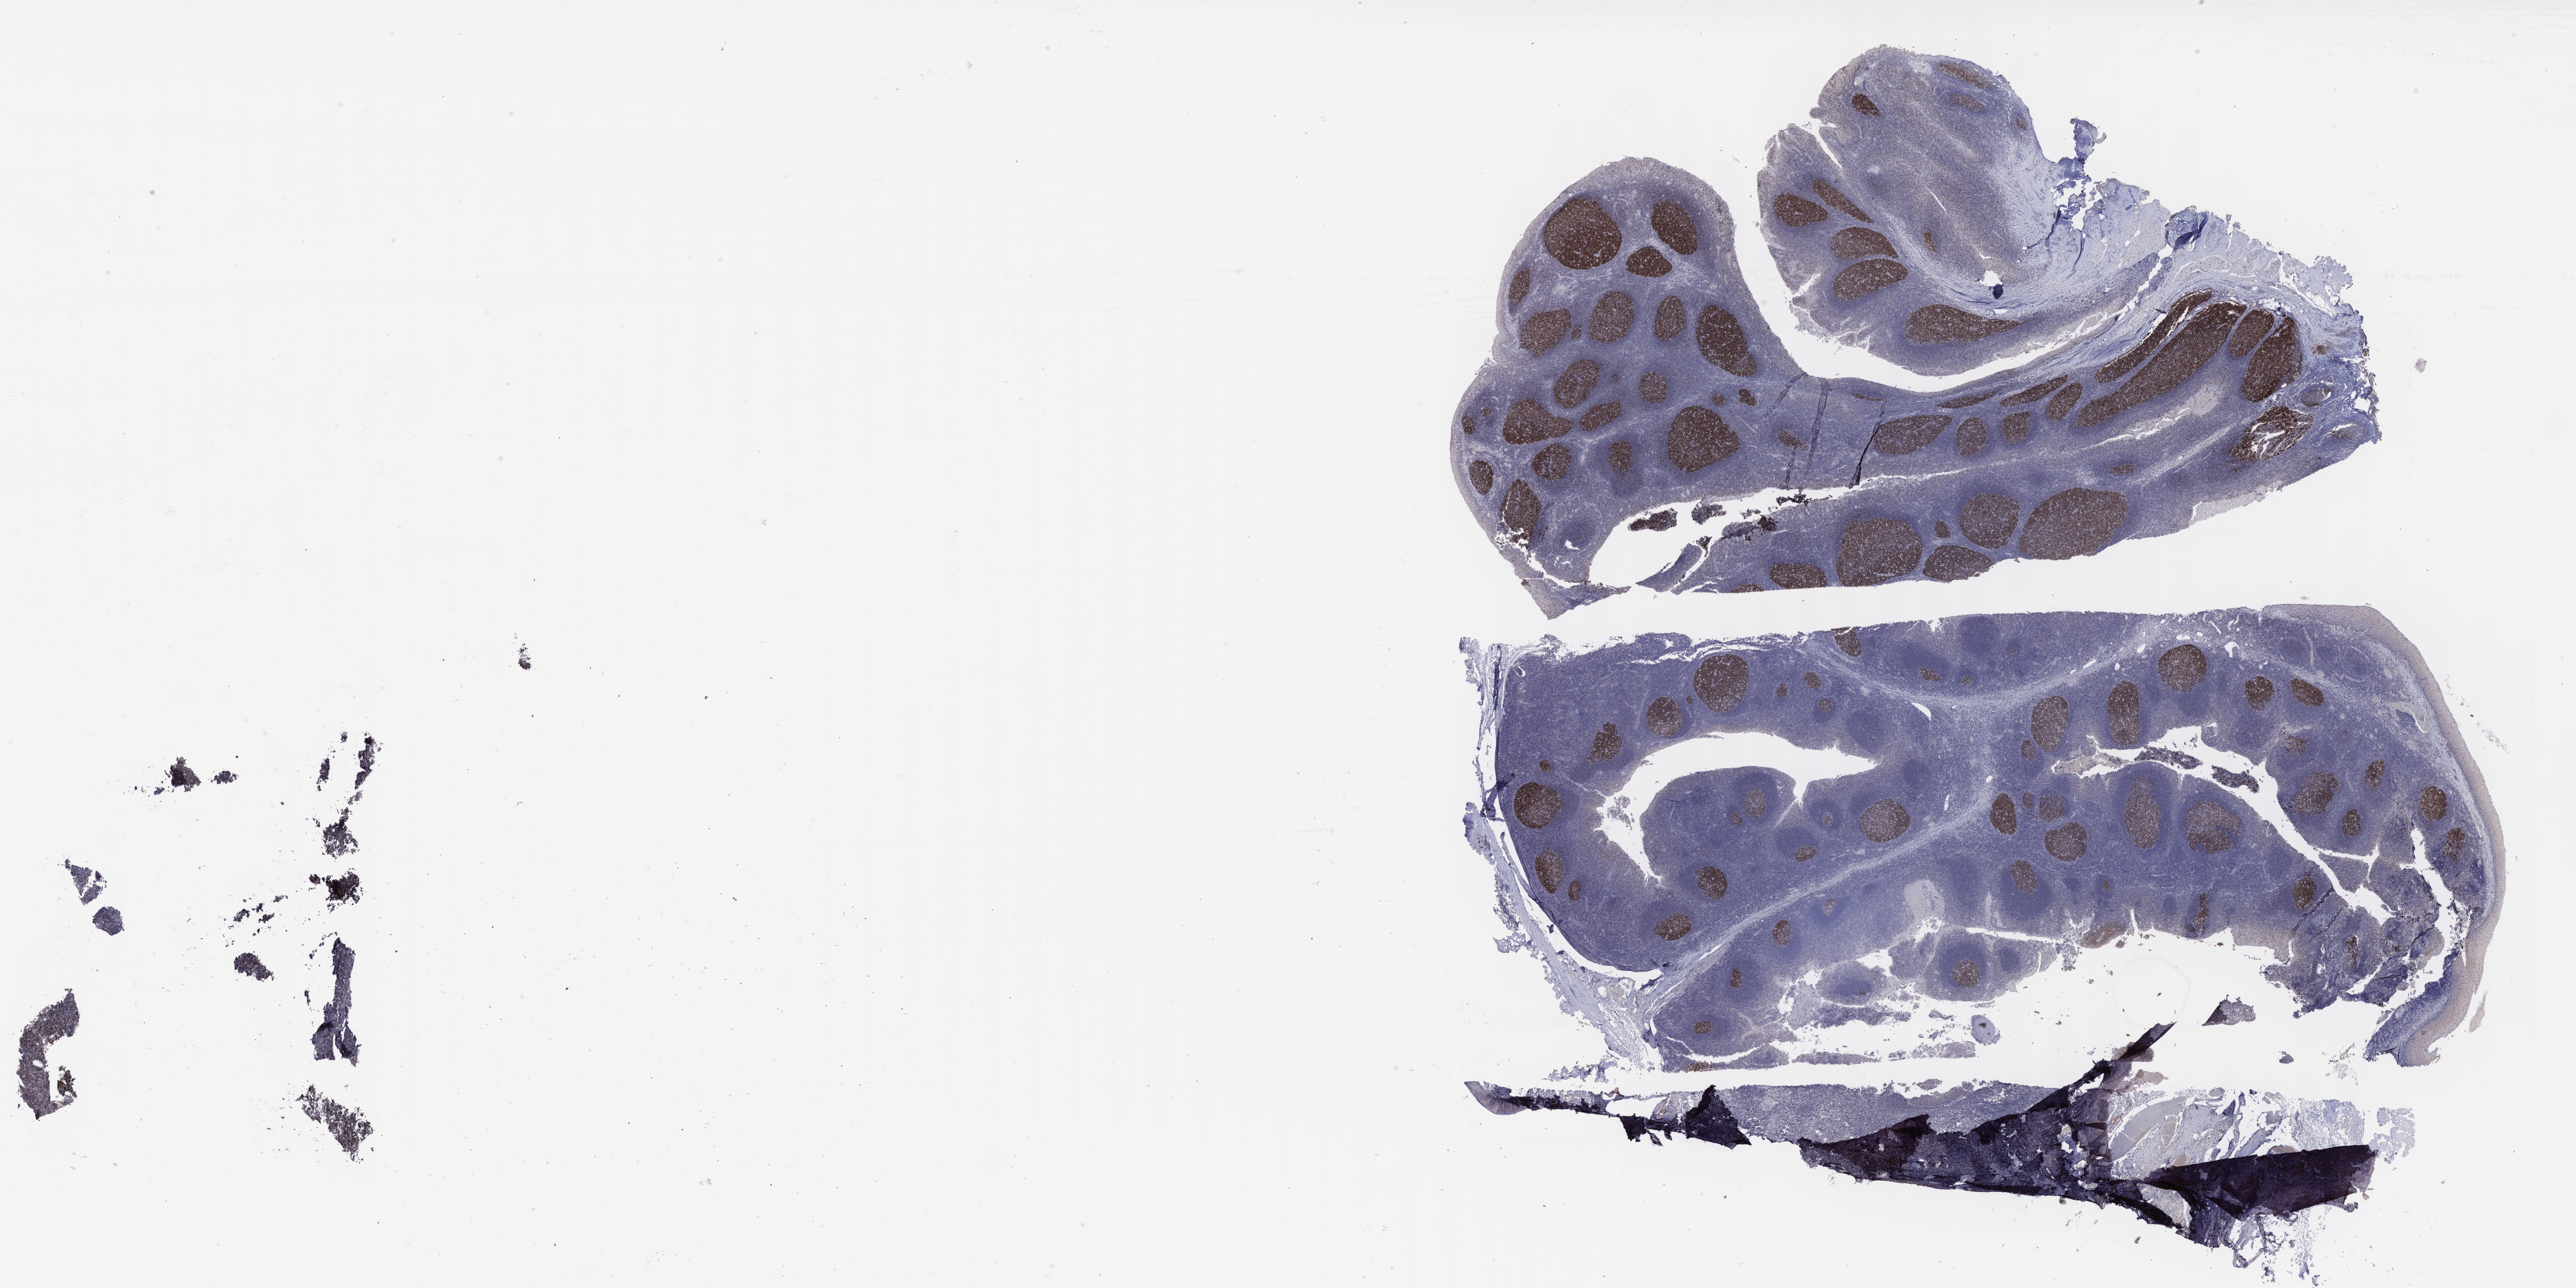
Immunohistochemistry (IHC) whole-slide image stained for BCL6 — low-resolution overview of the scanned area, about 31.2 x 15.6 mm. Tumor tissue. Anatomic site: peritoneum. Patient: female, age at initial diagnosis 6 years.
• diagnosis: Burkitt lymphoma, NOS